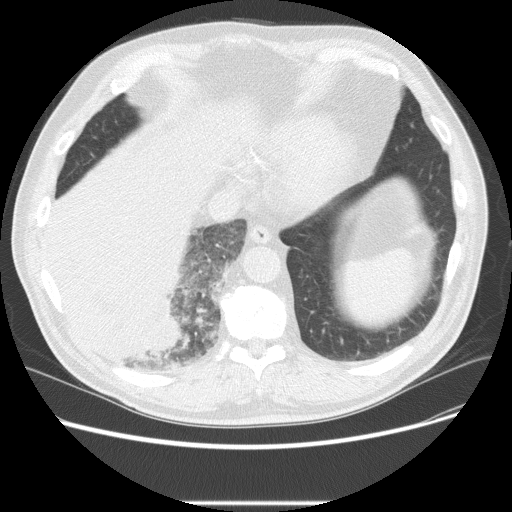
Low-dose screening chest CT, one axial slice. Position 56 of 233 along the scan axis. Reconstruction kernel STANDARD. 120 kVp. Lung window (W 1500 / L -600 HU). 512 × 512 image matrix.
Outlined on this slice (manually delineated by an expert):
- lesion 3 (tumor, lower lobe of right lung): box from (x=62, y=290) to (x=181, y=365) px